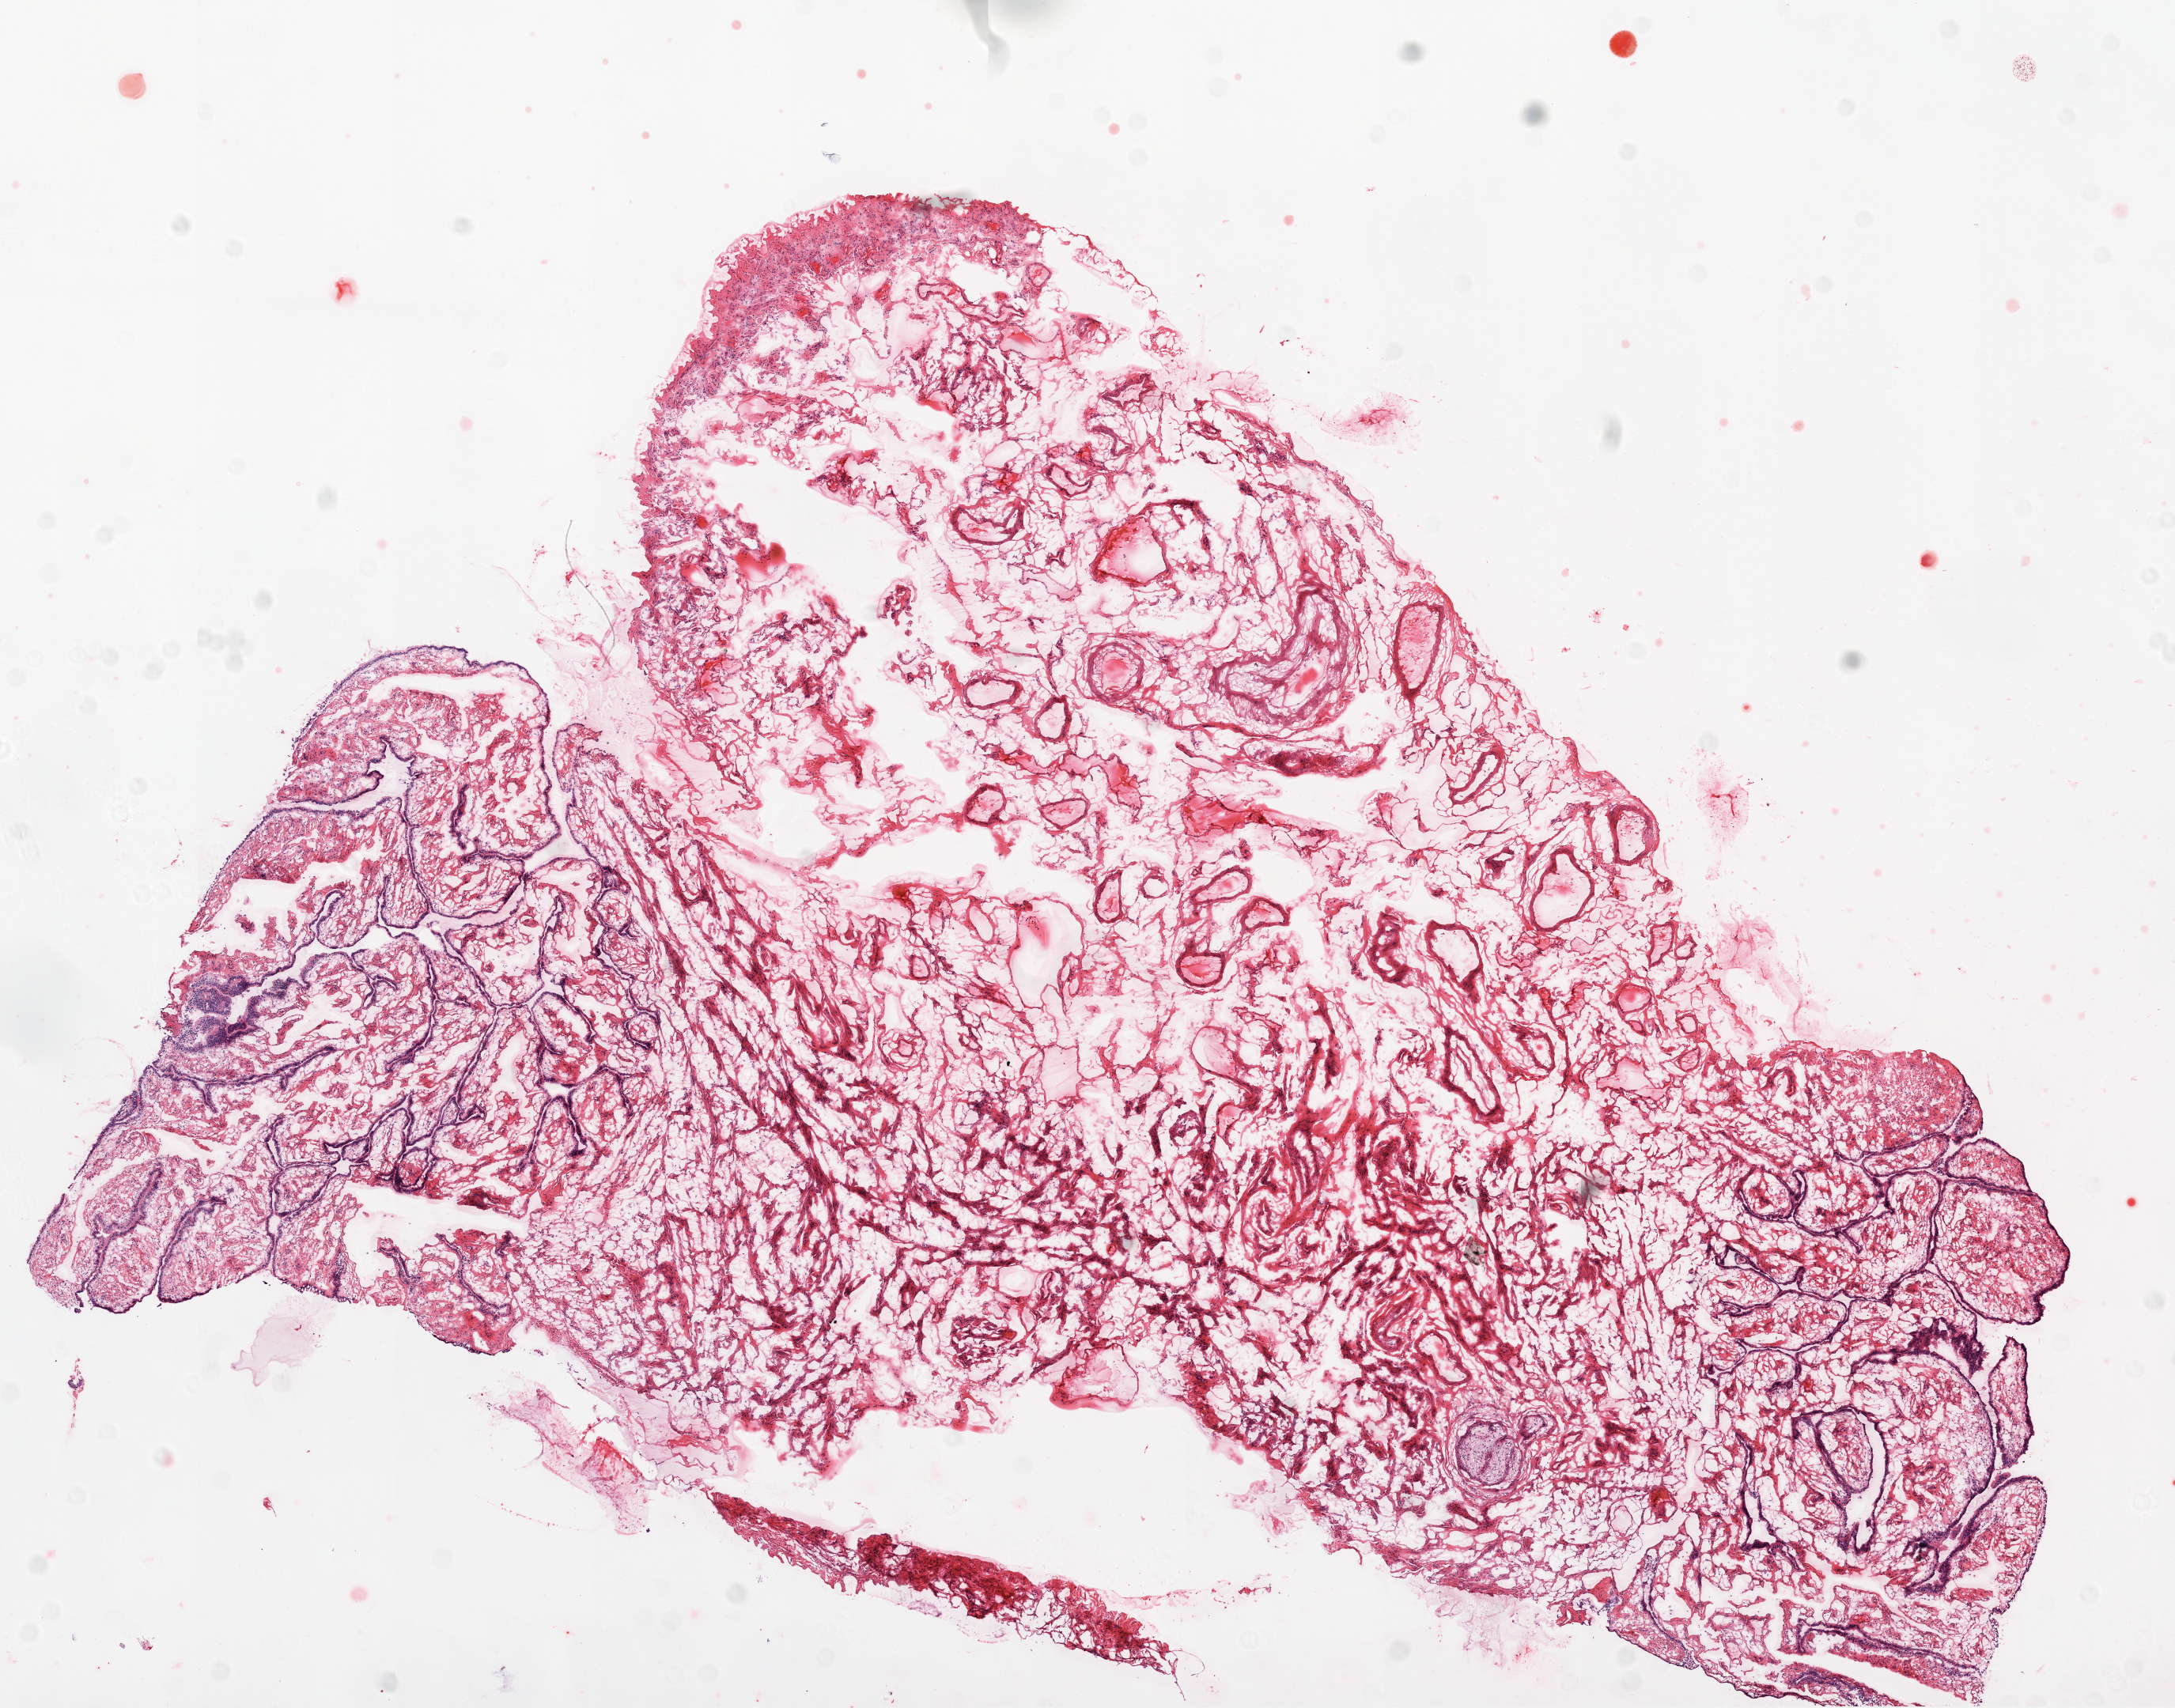
Whole-slide histology image, H&E-stained, whole scanned area (about 11.0 x 8.7 mm) shown as a low-resolution overview. Frozen section. Solid tissue normal (non-tumour tissue) sample from the ovary. Female, age 50 years at initial diagnosis.
This section: solid tissue normal sample (biorepository sample class). Patient diagnosis: Serous cystadenocarcinoma, NOS.